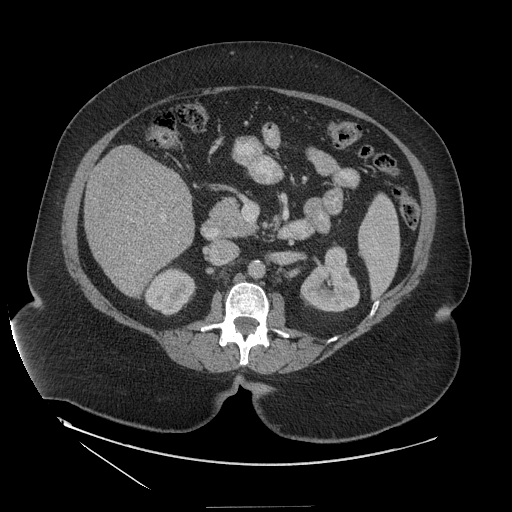
Contrast-enhanced abdominal CT (liver protocol), one axial slice; position 53 of 127 along the scan axis; reconstruction kernel STANDARD; 140 kVp; soft-tissue window (W 400 / L 40 HU); 512 × 512 image matrix, field of view 480 × 480 mm. From the clinical record (not read from this slice): diagnosis: hepatocellular carcinoma (patient treated with transarterial chemoembolisation; whether this scan precedes or follows treatment is not stated here); TNM stage (as recorded): Stage-II; Child-Pugh class: A; tumour differentiation: well differentiated; tumour nodularity: multinodular.
Structures marked on this image (semi-automatic segmentation, software-assisted and operator-edited):
- liver parenchyma outside the tumour (the mass and vessels are separate outlines, so this box may not span the whole liver): bounding box [x1, y1, x2, y2] px = [84, 146, 194, 296]